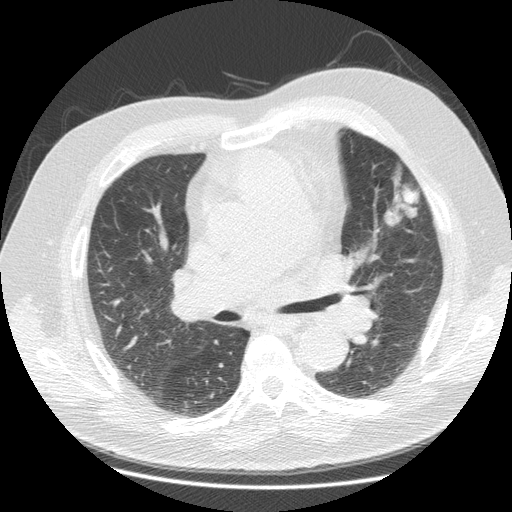
Chest CT (low-dose screening protocol), one axial image; second annual screen; lung window (W 1500 / L -600 HU); 2.5 mm slice thickness; standard (soft-tissue) reconstruction kernel (STANDARD); 512 × 512 image matrix. Male participant, aged 67 years at enrolment.
- Lesion marked by an expert reader, bounding box [x1, y1, x2, y2] px = [366, 164, 436, 232].
- The screening reader recorded 3 non-calcified nodules or masses ≥4 mm on this exam (left upper lobe, left upper lobe, left upper lobe); which of them this box marks is not recorded.